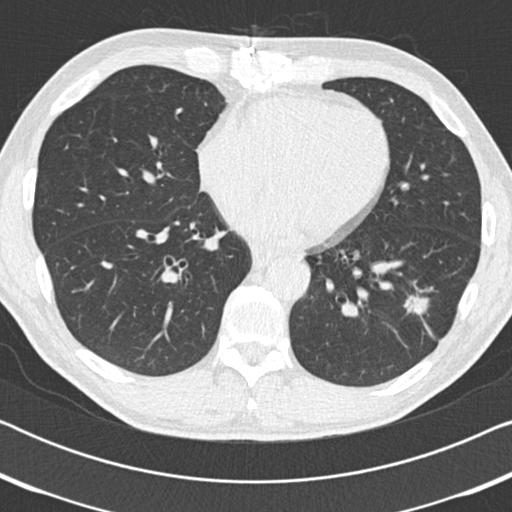
Low-dose screening chest CT, one axial slice; position 75 of 186 along the scan axis; reconstruction kernel B30f; lung window (W 1500 / L -600 HU); 512 × 512 image matrix, field of view 330 × 330 mm.
Structures marked on this image (expert manual segmentation):
- lesion 1 (tumor, lower lobe of left lung): bounding box [x1, y1, x2, y2] px = [405, 295, 429, 314]